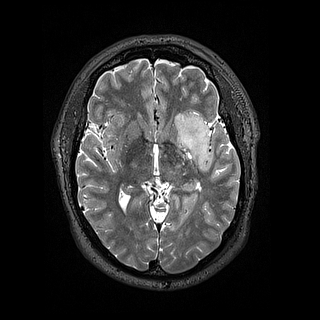
Brain MRI from a brain-tumour surgery series, one axial slice. Slice 88 of 144 in the series (ordered by position). 1.2 mm slice thickness. 320 × 320 image matrix, field of view 254 × 254 mm. From the clinical record (not read from this slice): histopathology: Astrocytoma; WHO grade: 2; IDH mutation: yes.
Annotated regions visible in this slice (expert manual segmentation):
- tumour: bounding box (x1, y1, x2, y2) in pixels: (174, 108, 210, 171)